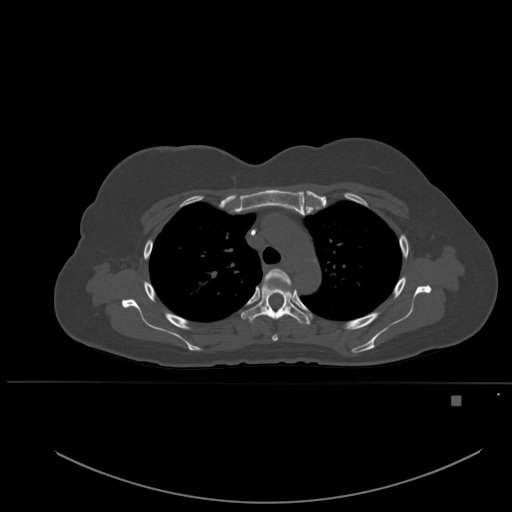
CT including the spine, one axial slice. Slice 383 of 651 in the series (ordered by position). Bone window (W 1800 / L 400 HU). 1.5 mm slice thickness. 512 × 512 image matrix. Patient: female, 49 years. Case-level facts recorded for this patient, not image findings: primary cancer: breast.
Annotated regions visible in this slice (semi-automatically segmented with operator editing):
- T3 vertebra: bounding box [x1, y1, x2, y2] px = [264, 268, 291, 341]
- T4 vertebra: [241, 282, 310, 325]